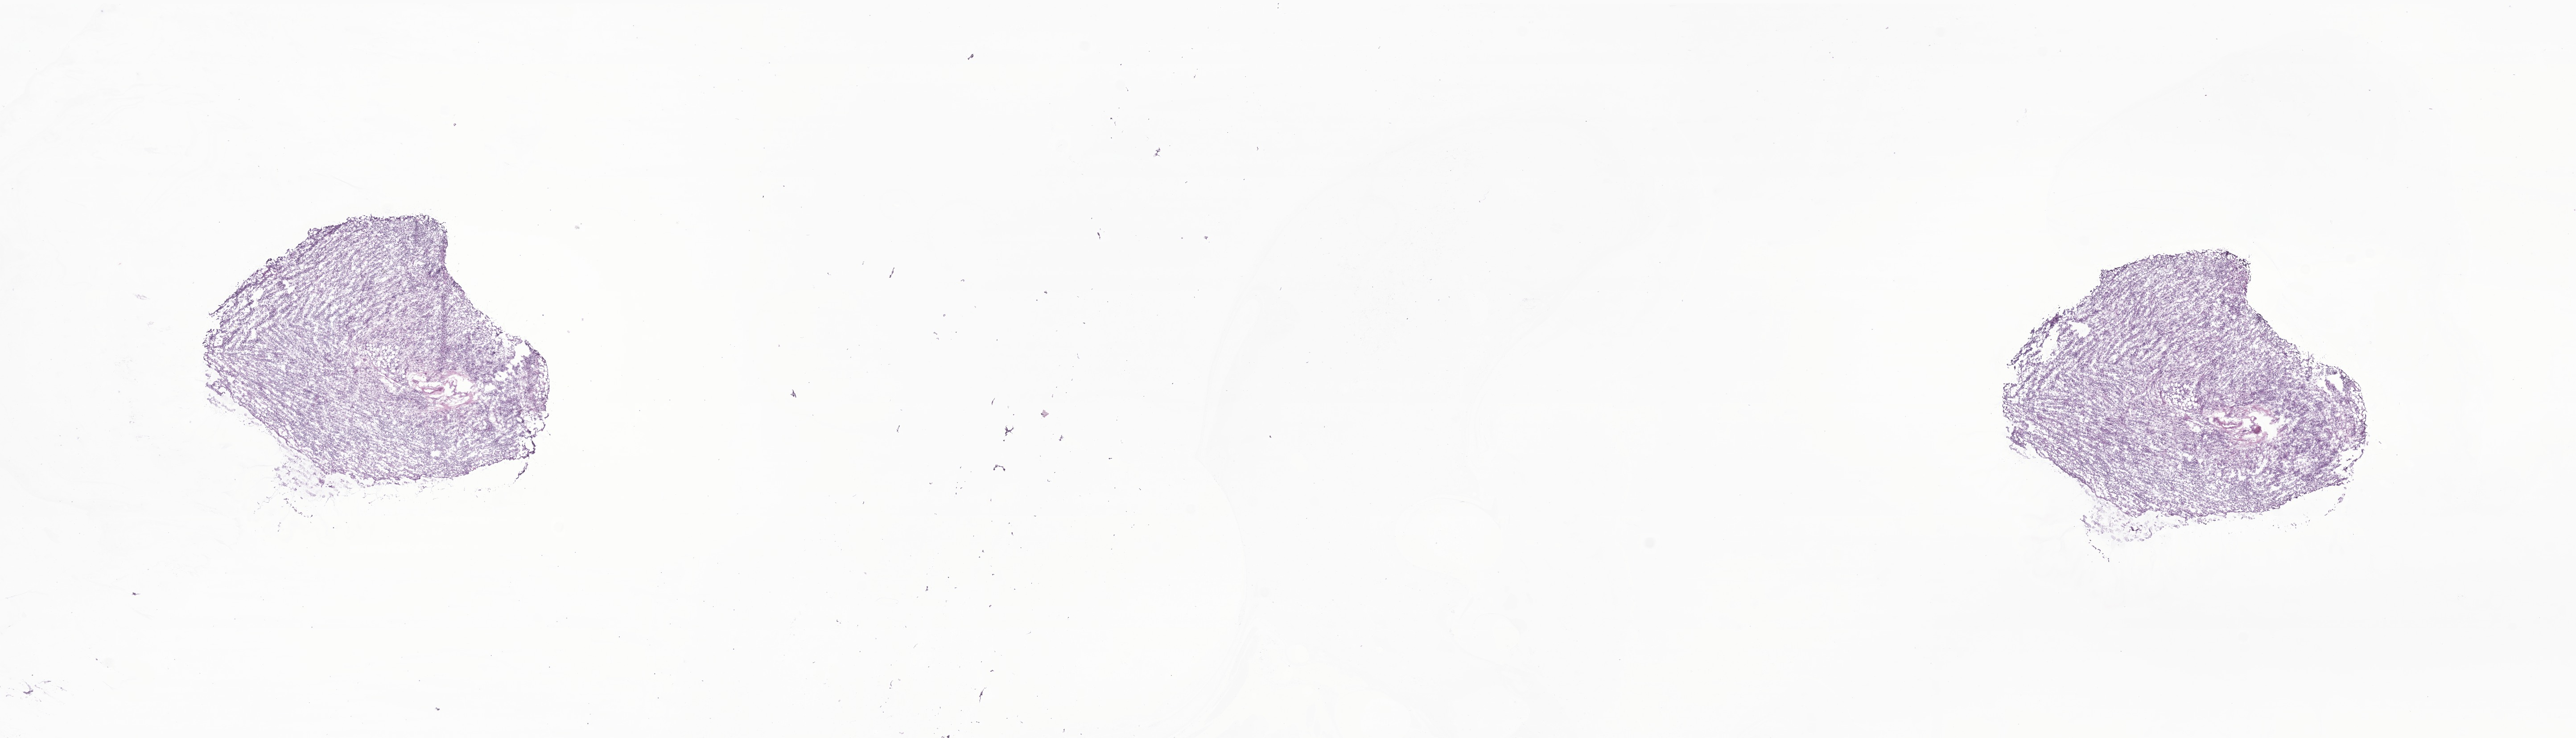
Whole-slide image, H&E stain of tumor tissue from the peritoneum — whole scanned area (about 24.4 x 7.0 mm) shown as a low-resolution overview; frozen section (OCT-embedded). Patient male; age 614 days (about 1.7 years).
Diagnosis (ICD-O-3 morphology term): Embryonal rhabdomyosarcoma, NOS.